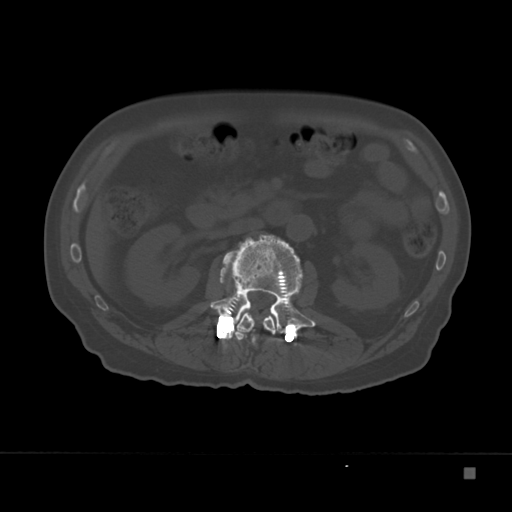
CT including the spine, one axial slice. Slice 96 of 332 in the series (ordered by position). Reconstruction kernel Br40s. Bone window (W 1800 / L 400 HU). 512 × 512 image matrix. Male patient, age 72 years. From the clinical record (not read from this slice): primary cancer: skeletal.
Outlined on this slice (semi-automatically segmented with operator editing):
- L1 vertebra: box from (x=231, y=310) to (x=277, y=335) px
- L2 vertebra: (x=209, y=237)–(x=316, y=333)